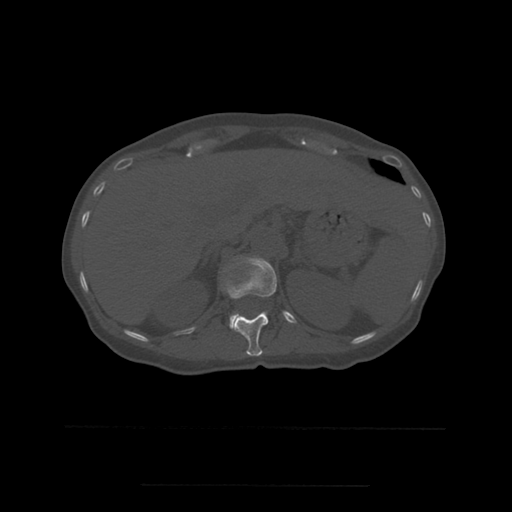
CT including the spine, one axial slice; slice 252 of 544 in the series (ordered by position); bone window (W 1800 / L 400 HU); 1.25 mm slice thickness; 512 × 512 image matrix, field of view 350 × 350 mm. Patient age 58 years. From the clinical record (not read from this slice): primary cancer: lung.
Outlined on this slice (semi-automatically segmented with operator editing):
- L1 vertebra: bounding box (x1, y1, x2, y2) in pixels: (230, 314, 238, 331)
- T12 vertebra: (225, 257, 277, 357)